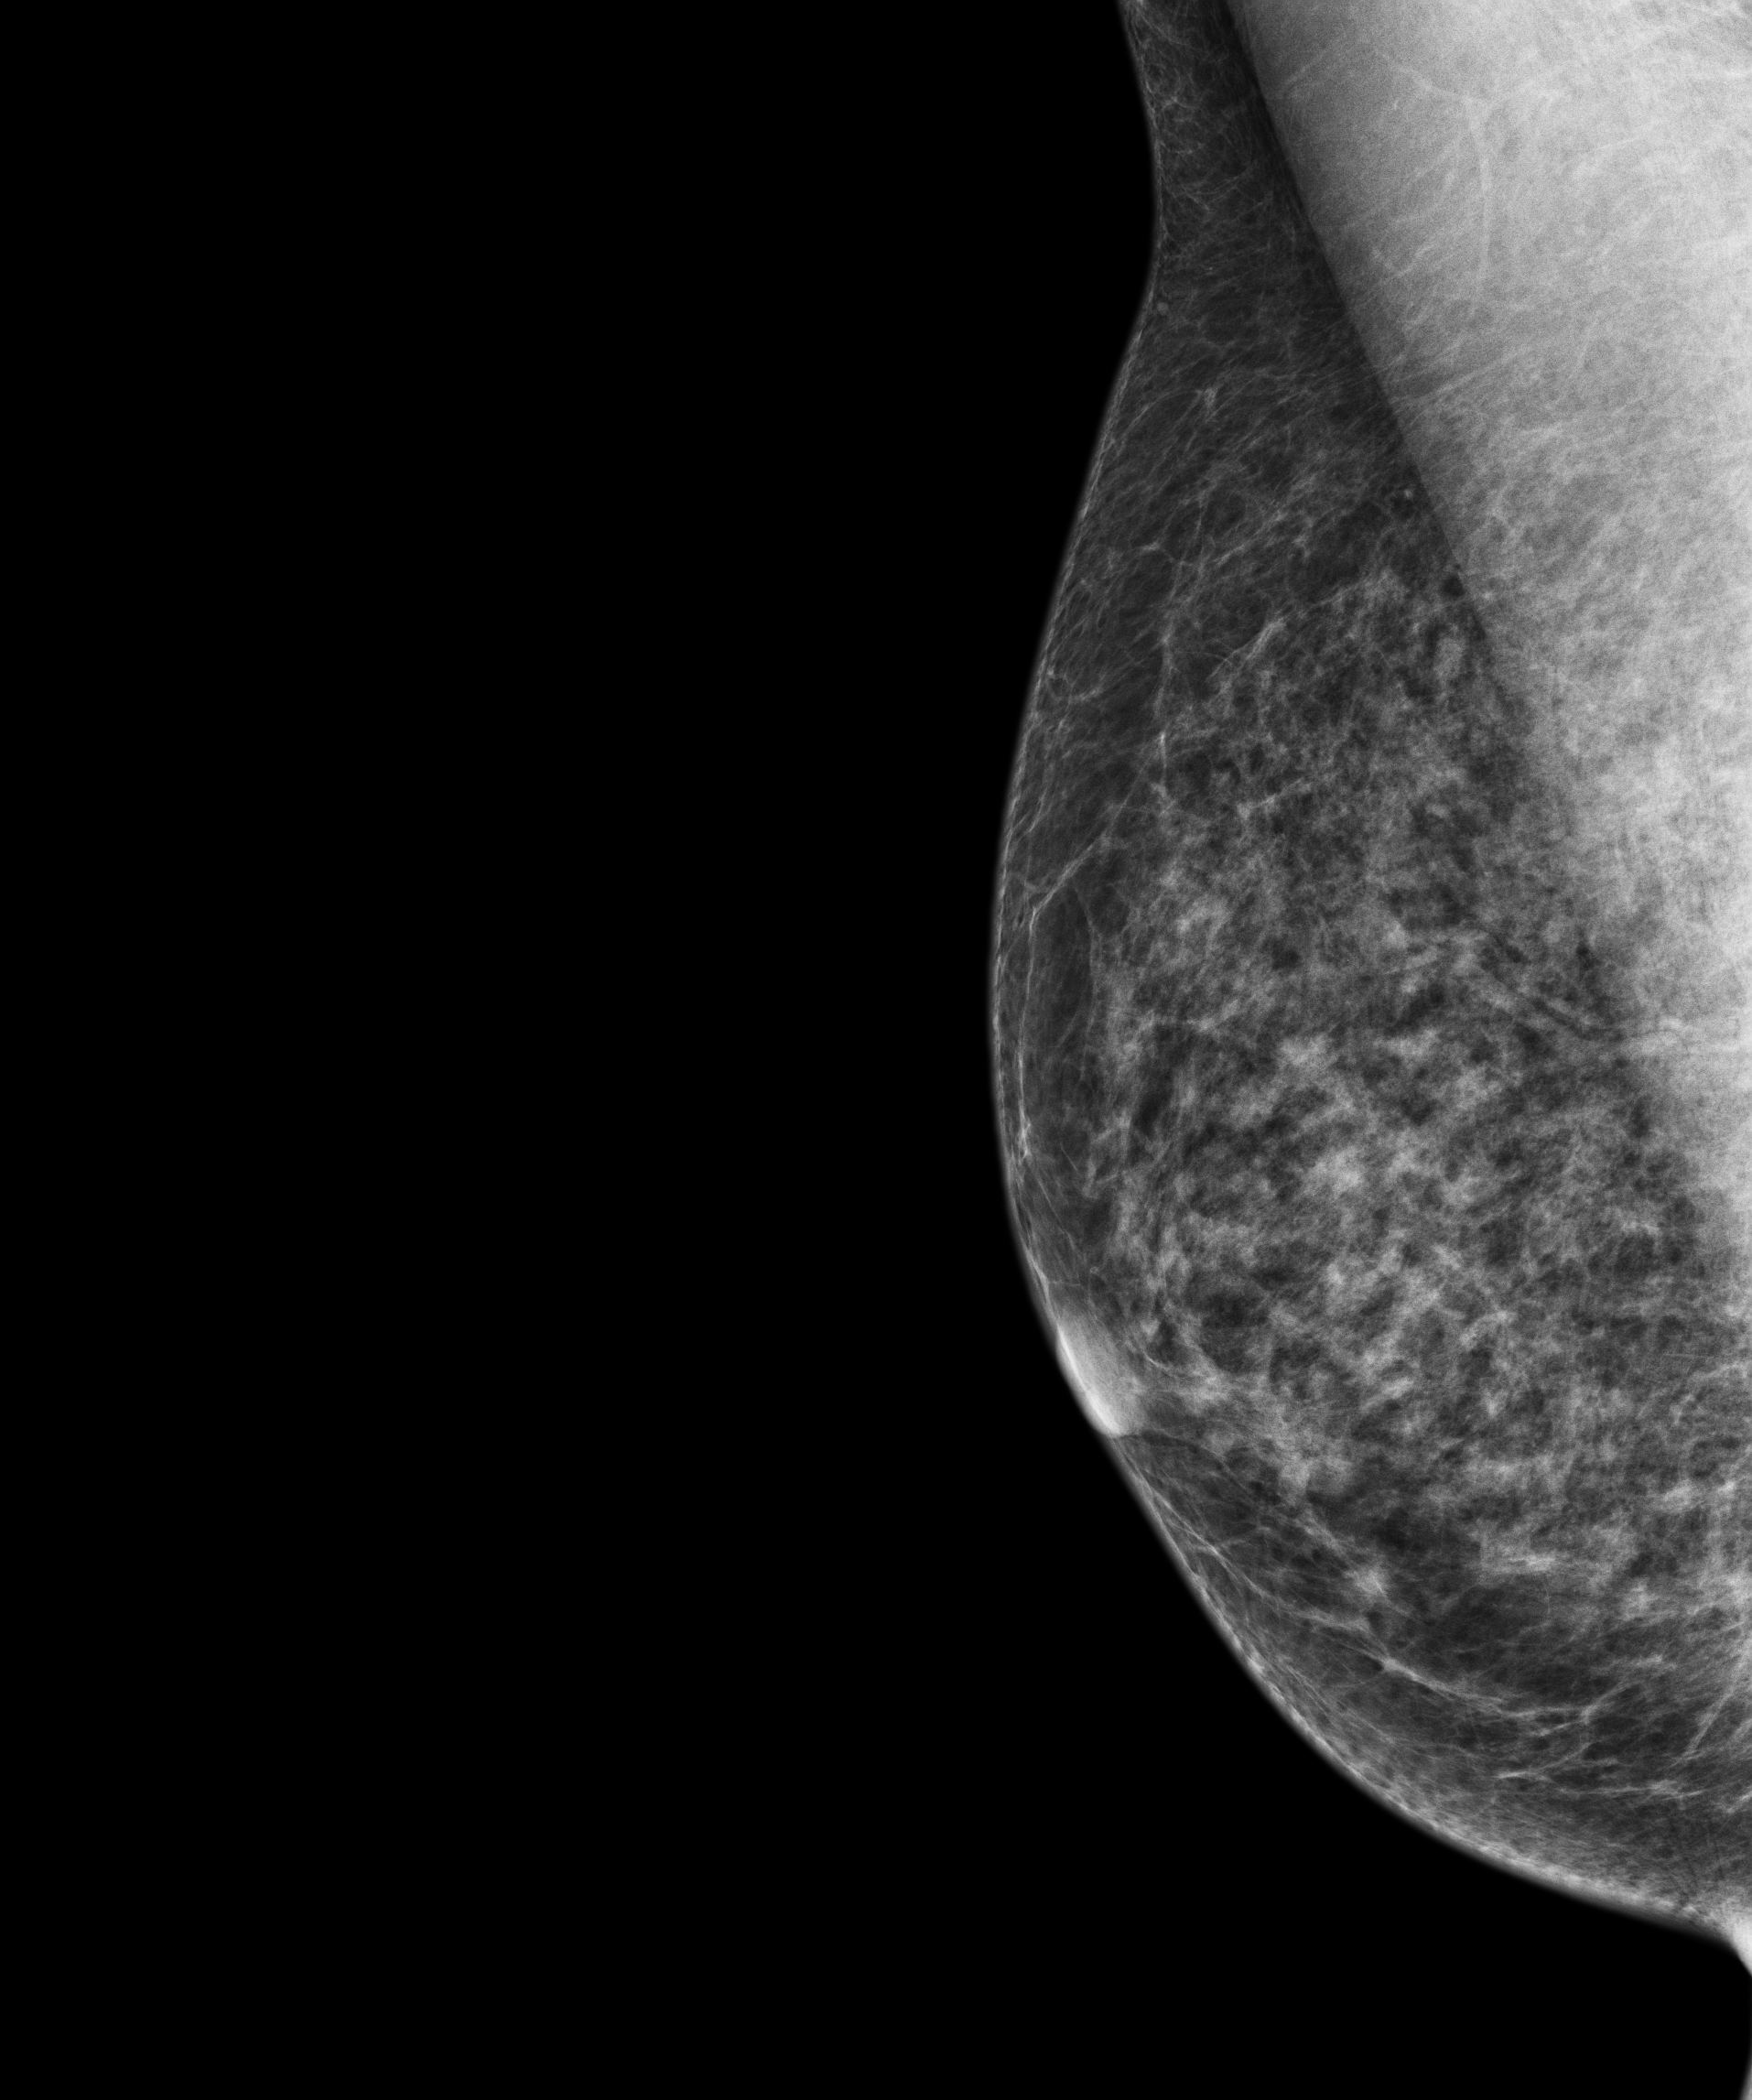
Digital mammogram (FFDM); right breast; mediolateral oblique (MLO) view; screening examination. Female patient, age 69 years.
- breast density at the screening exam (both breasts): heterogeneously dense (BI-RADS density category c)
- final BI-RADS assessment for this screening round (tomosynthesis exam, both breasts): category 1
- recall: no recall after this screen